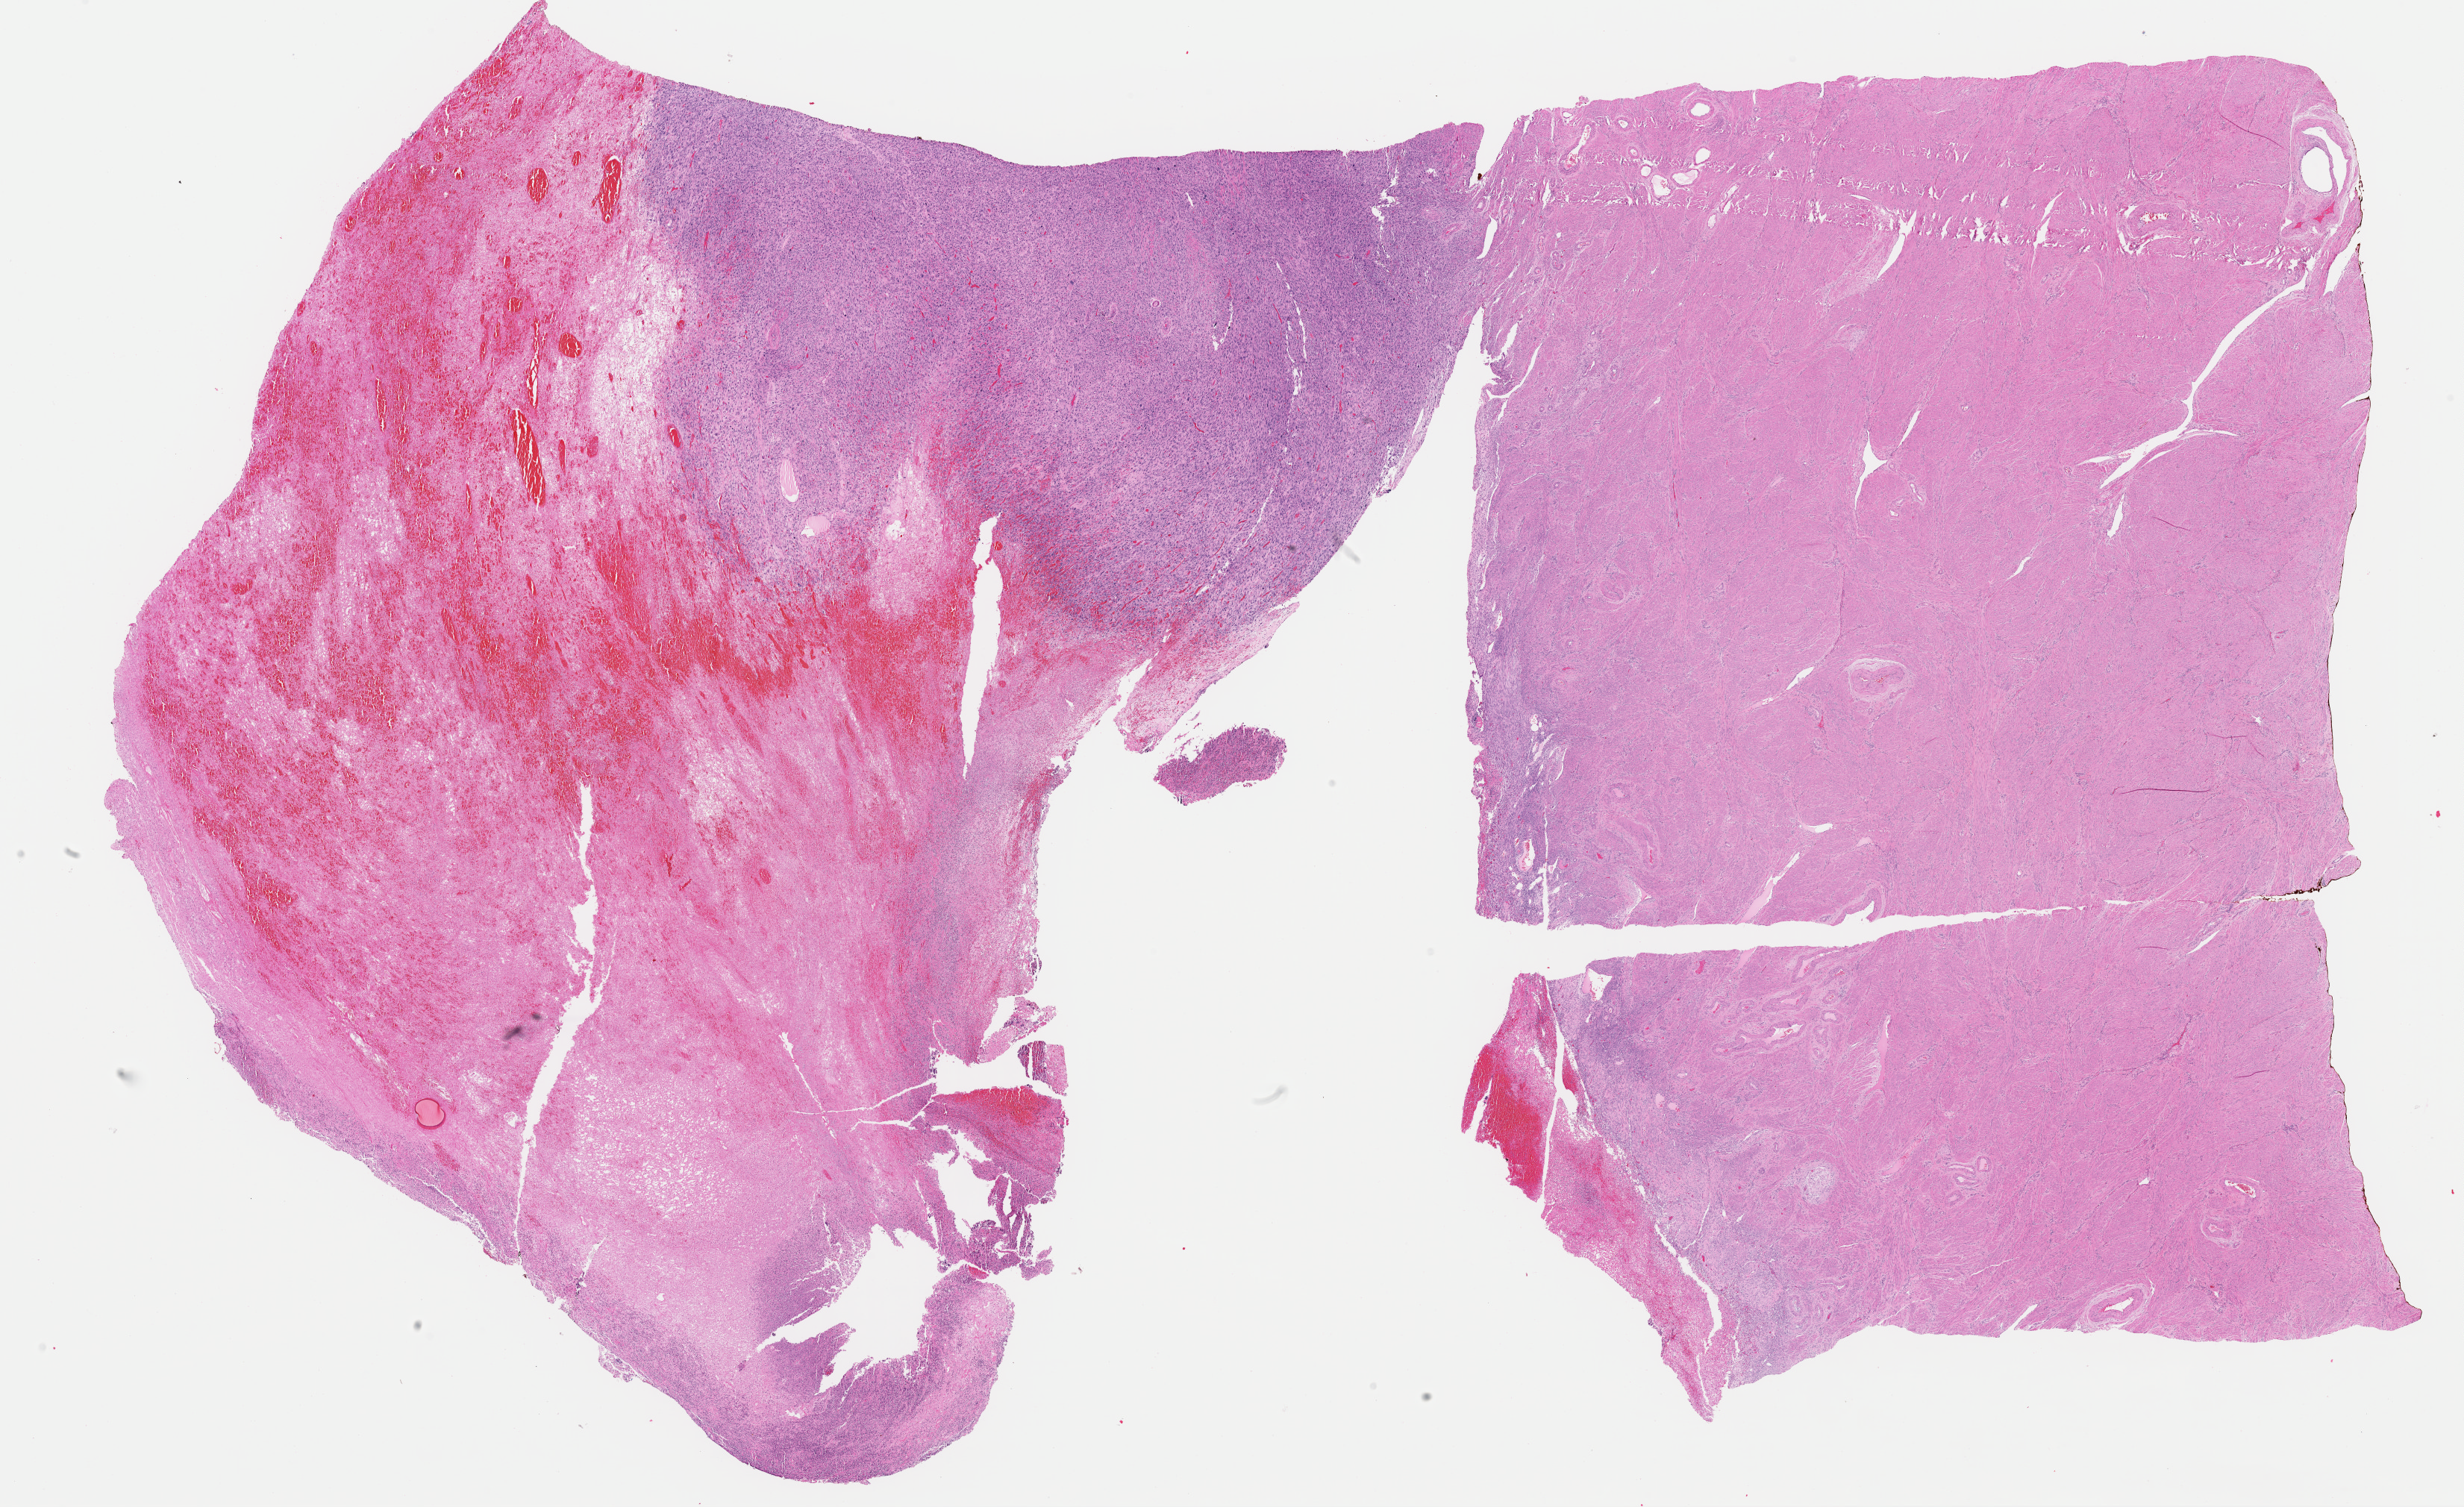
Digitized H&E-stained tissue section (whole slide), shown as a low-resolution overview of the whole scanned area (about 26.1 x 16.0 mm, from a 40x scan); FFPE section; primary tumour sample from the uterus. Female patient; age at initial diagnosis 41 years.
Diagnosis: Leiomyosarcoma, NOS.